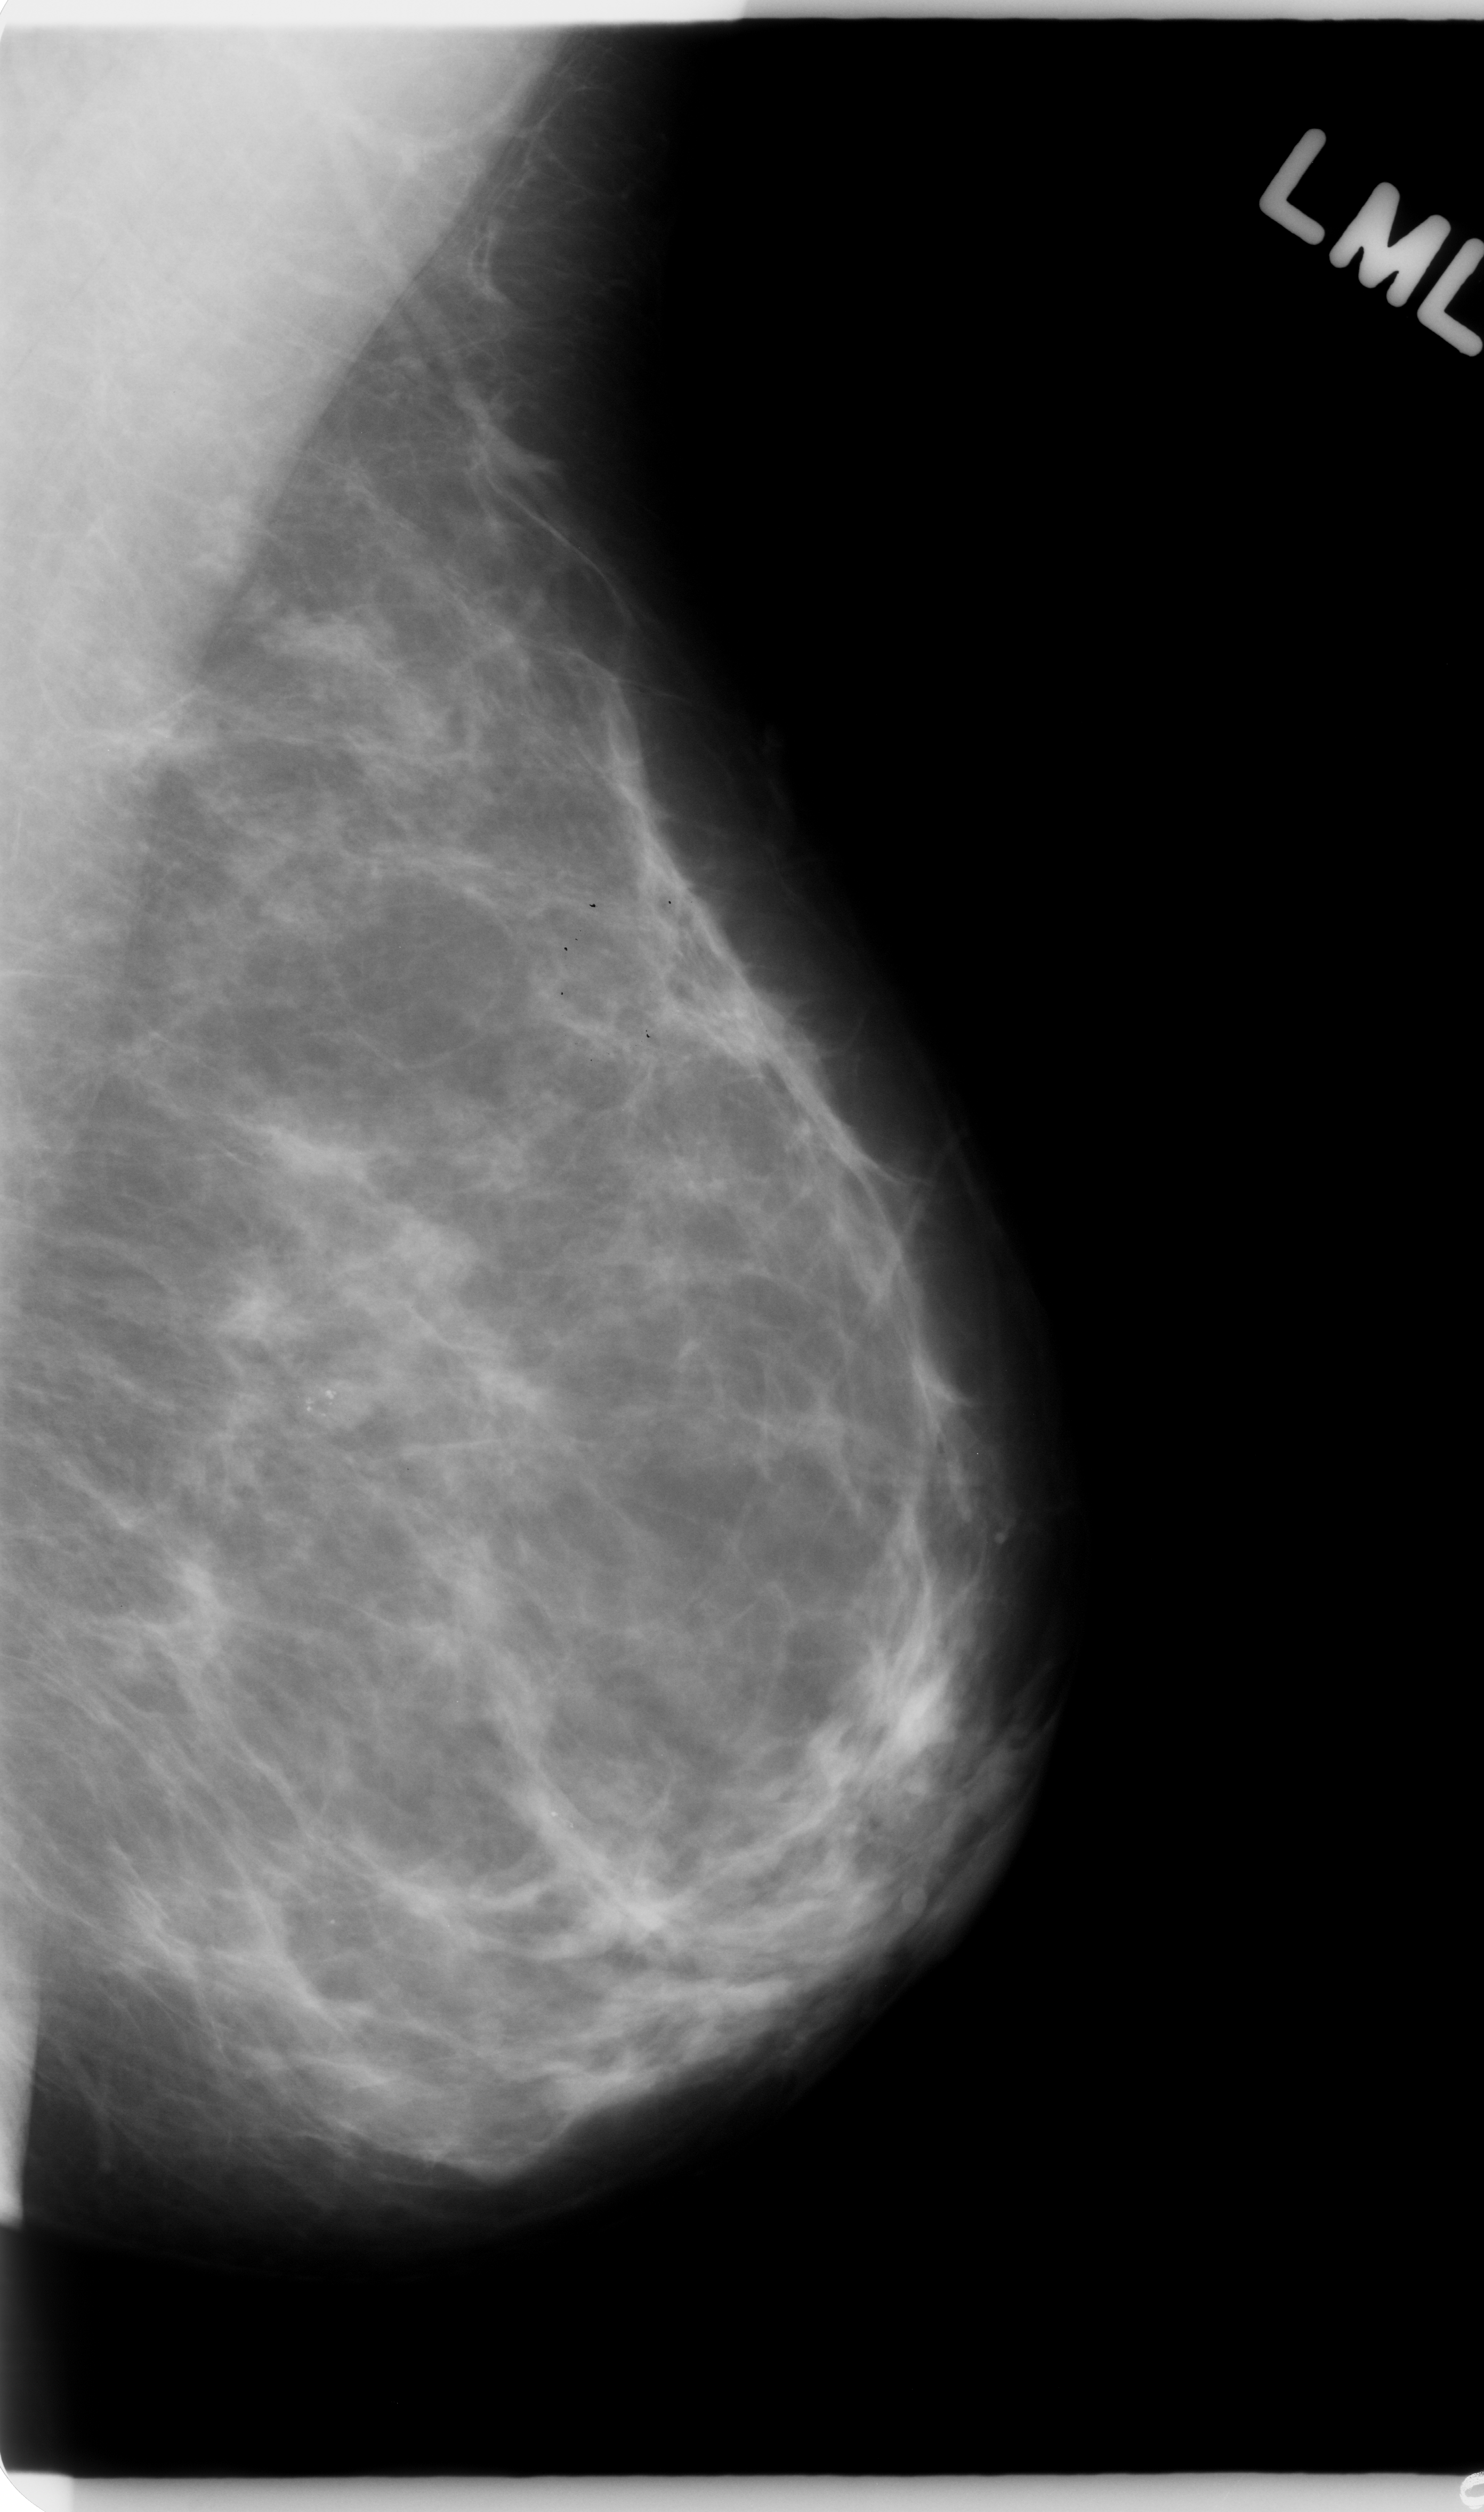
Mammogram (digitized film); left breast; MLO view; BI-RADS breast density category 2 (scale 1–4); 1484 × 2512 image matrix.
Marked abnormalities (boxes around the expert regions of interest):
- Finding 1 of 2: calcifications, morphology punctate, distribution clustered; BI-RADS assessment category 3; pathology (as recorded): benign: bounding box <255,1334,398,1498> (left, top, right, bottom; pixels)
- Finding 2 of 2: calcifications, morphology punctate, distribution clustered; BI-RADS assessment category 4; pathology (as recorded): benign: <464,1752,602,1912>